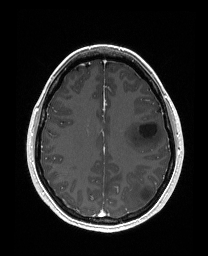
Brain MRI from a brain-tumour surgery series, one axial slice; position 107 of 176 along the scan axis; T1-weighted post-contrast; 208 × 256 image matrix. From the clinical record (not read from this slice): histopathology: Astrocytoma; WHO grade: 3; IDH mutation: yes; tumour location: Left Frontal.
Annotated regions visible in this slice (manually delineated by an expert):
- tumour: bounding box <123,119,163,152> (left, top, right, bottom; pixels)